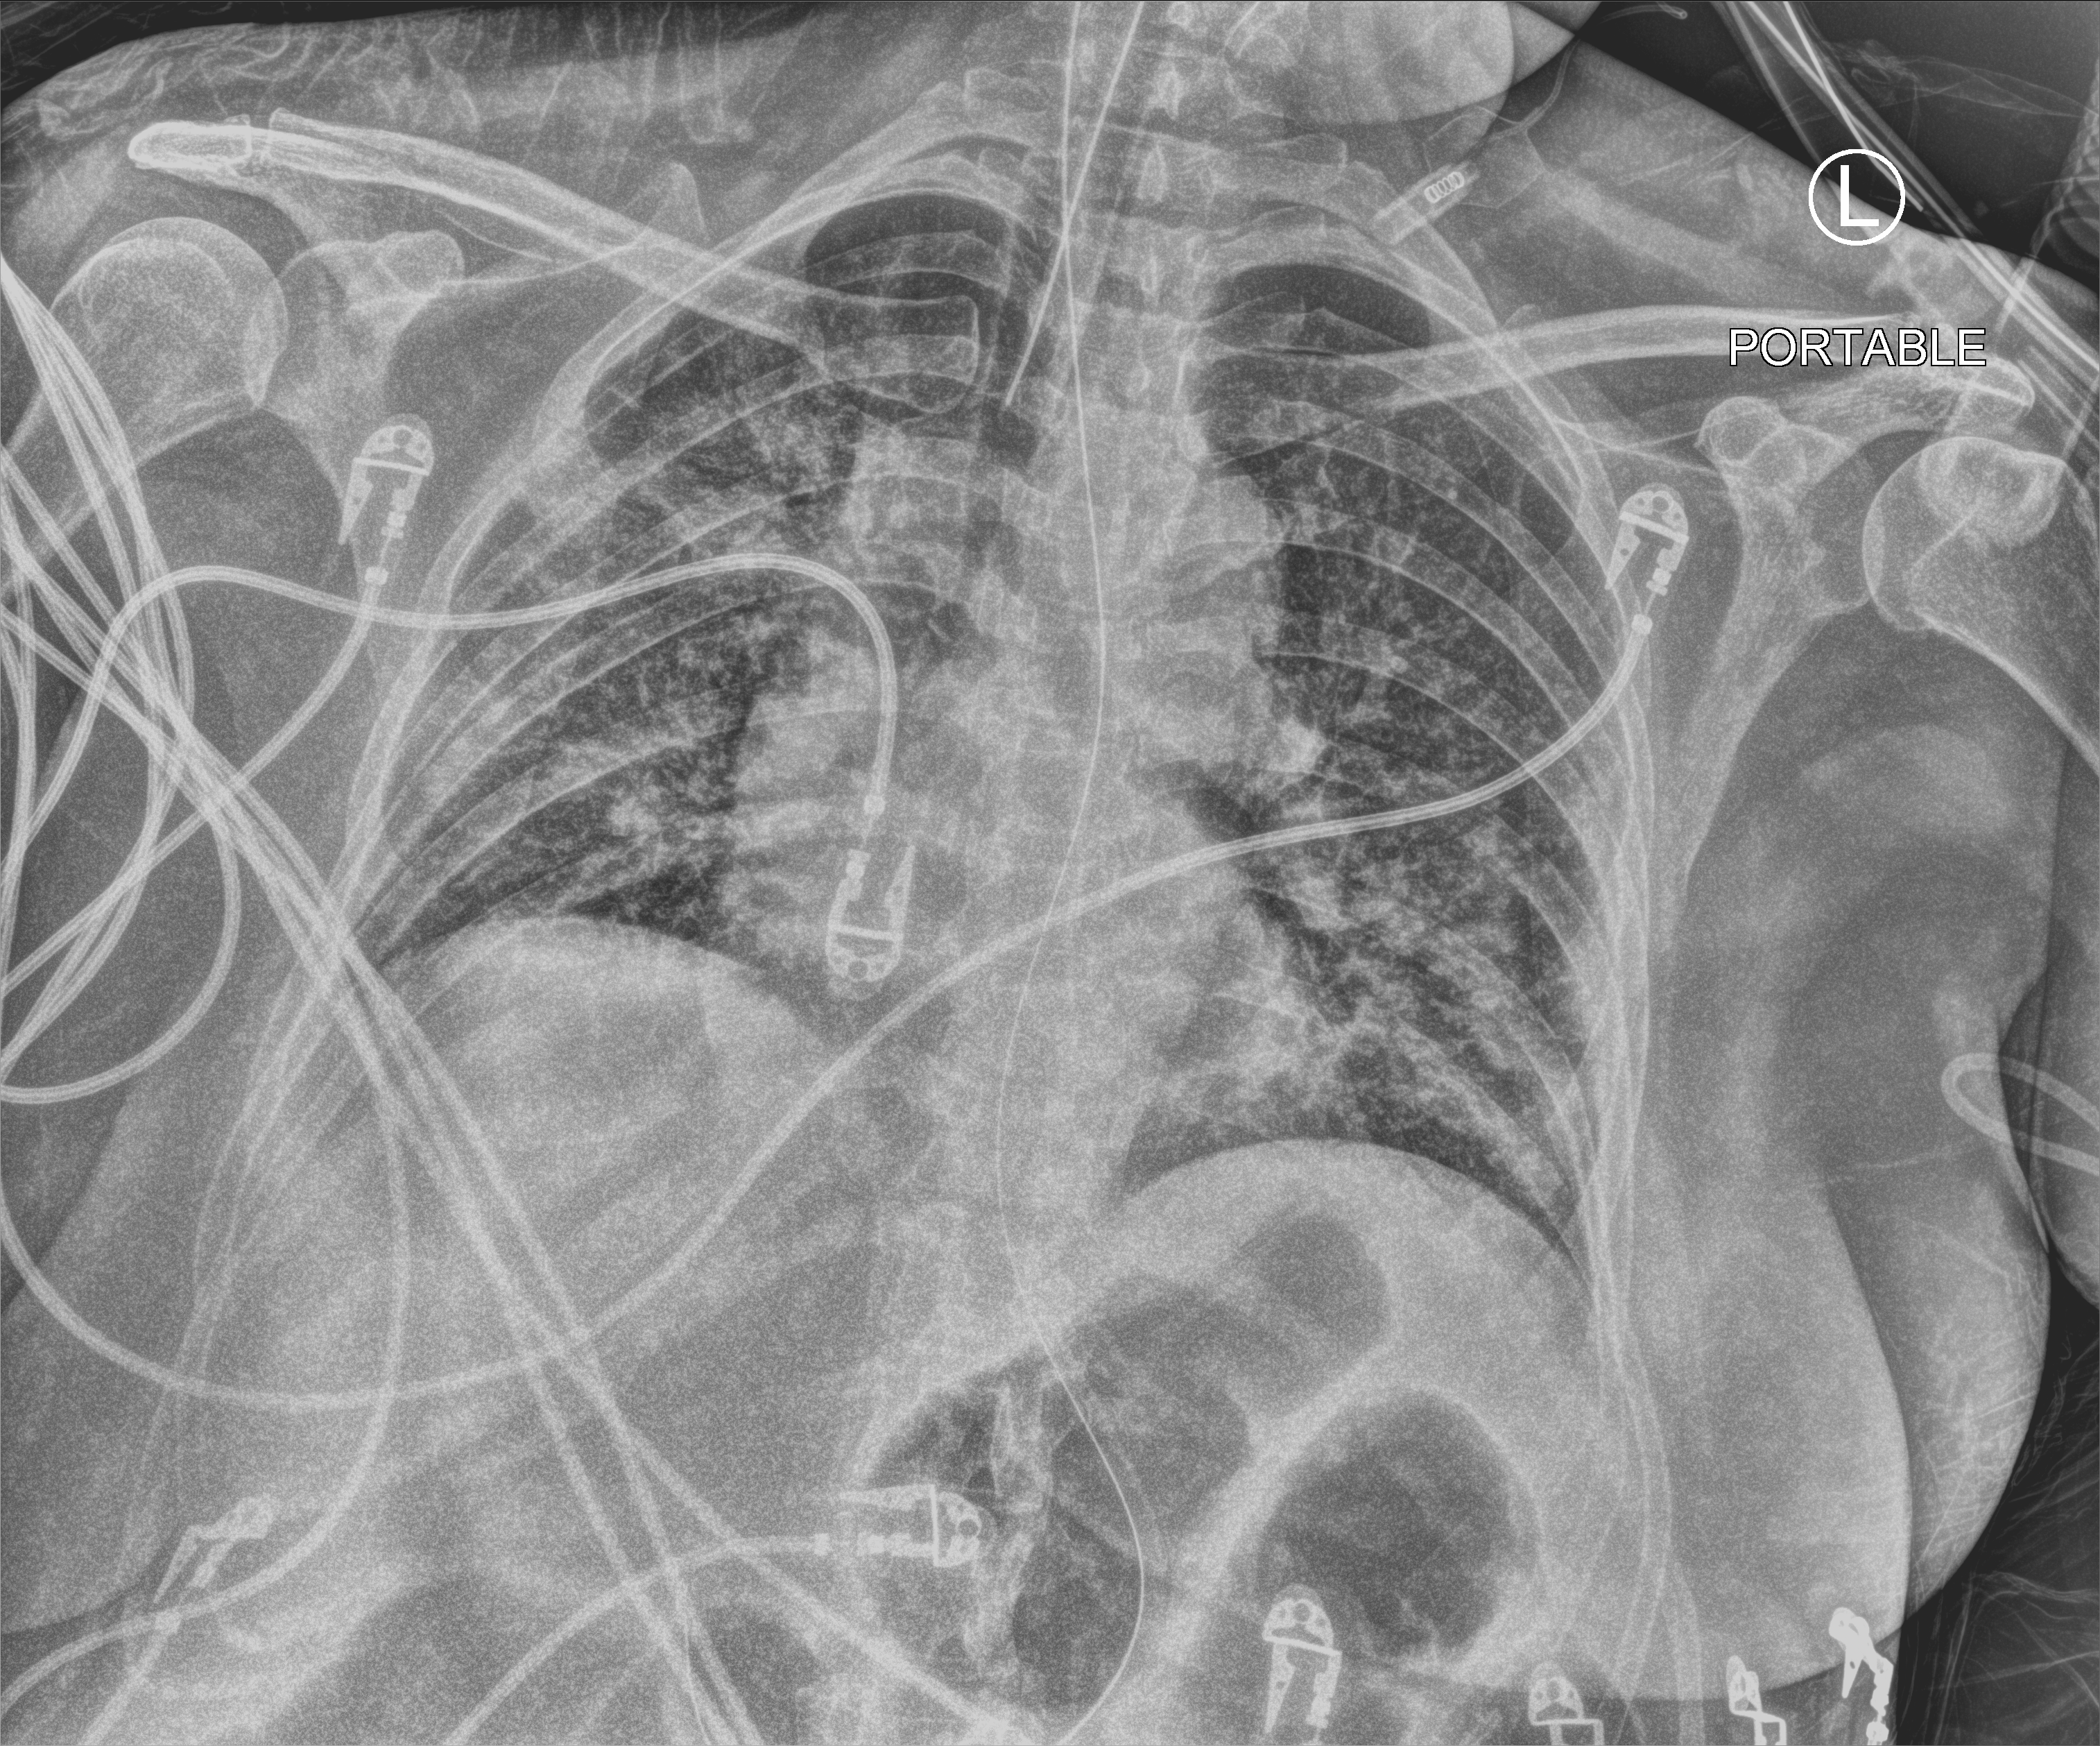
Portable chest radiograph, anteroposterior (AP) projection. Female patient hospitalised with COVID-19, age 18–59 years.
Hospital-stay facts (about this admission, not read from this image; timing relative to this image not recorded): mechanically ventilated during this hospital stay: yes; admitted to intensive care during this hospital stay: yes; hypertension (admission record): no.